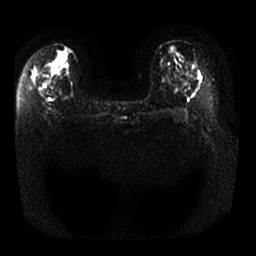
Breast MRI, one axial slice; position 11 of 25 along the scan axis; diffusion-weighted series; image 2 of 4 stored at this slice position (different b-values; order by instance number); 1.5 T; 4 mm slice thickness; 256 × 256 image matrix, field of view 340 × 340 mm. Female patient.
Annotated regions visible in this slice (manually delineated by an expert):
- tumour on diffusion-weighted imaging: bounding box [x1, y1, x2, y2] px = [36, 72, 50, 86]